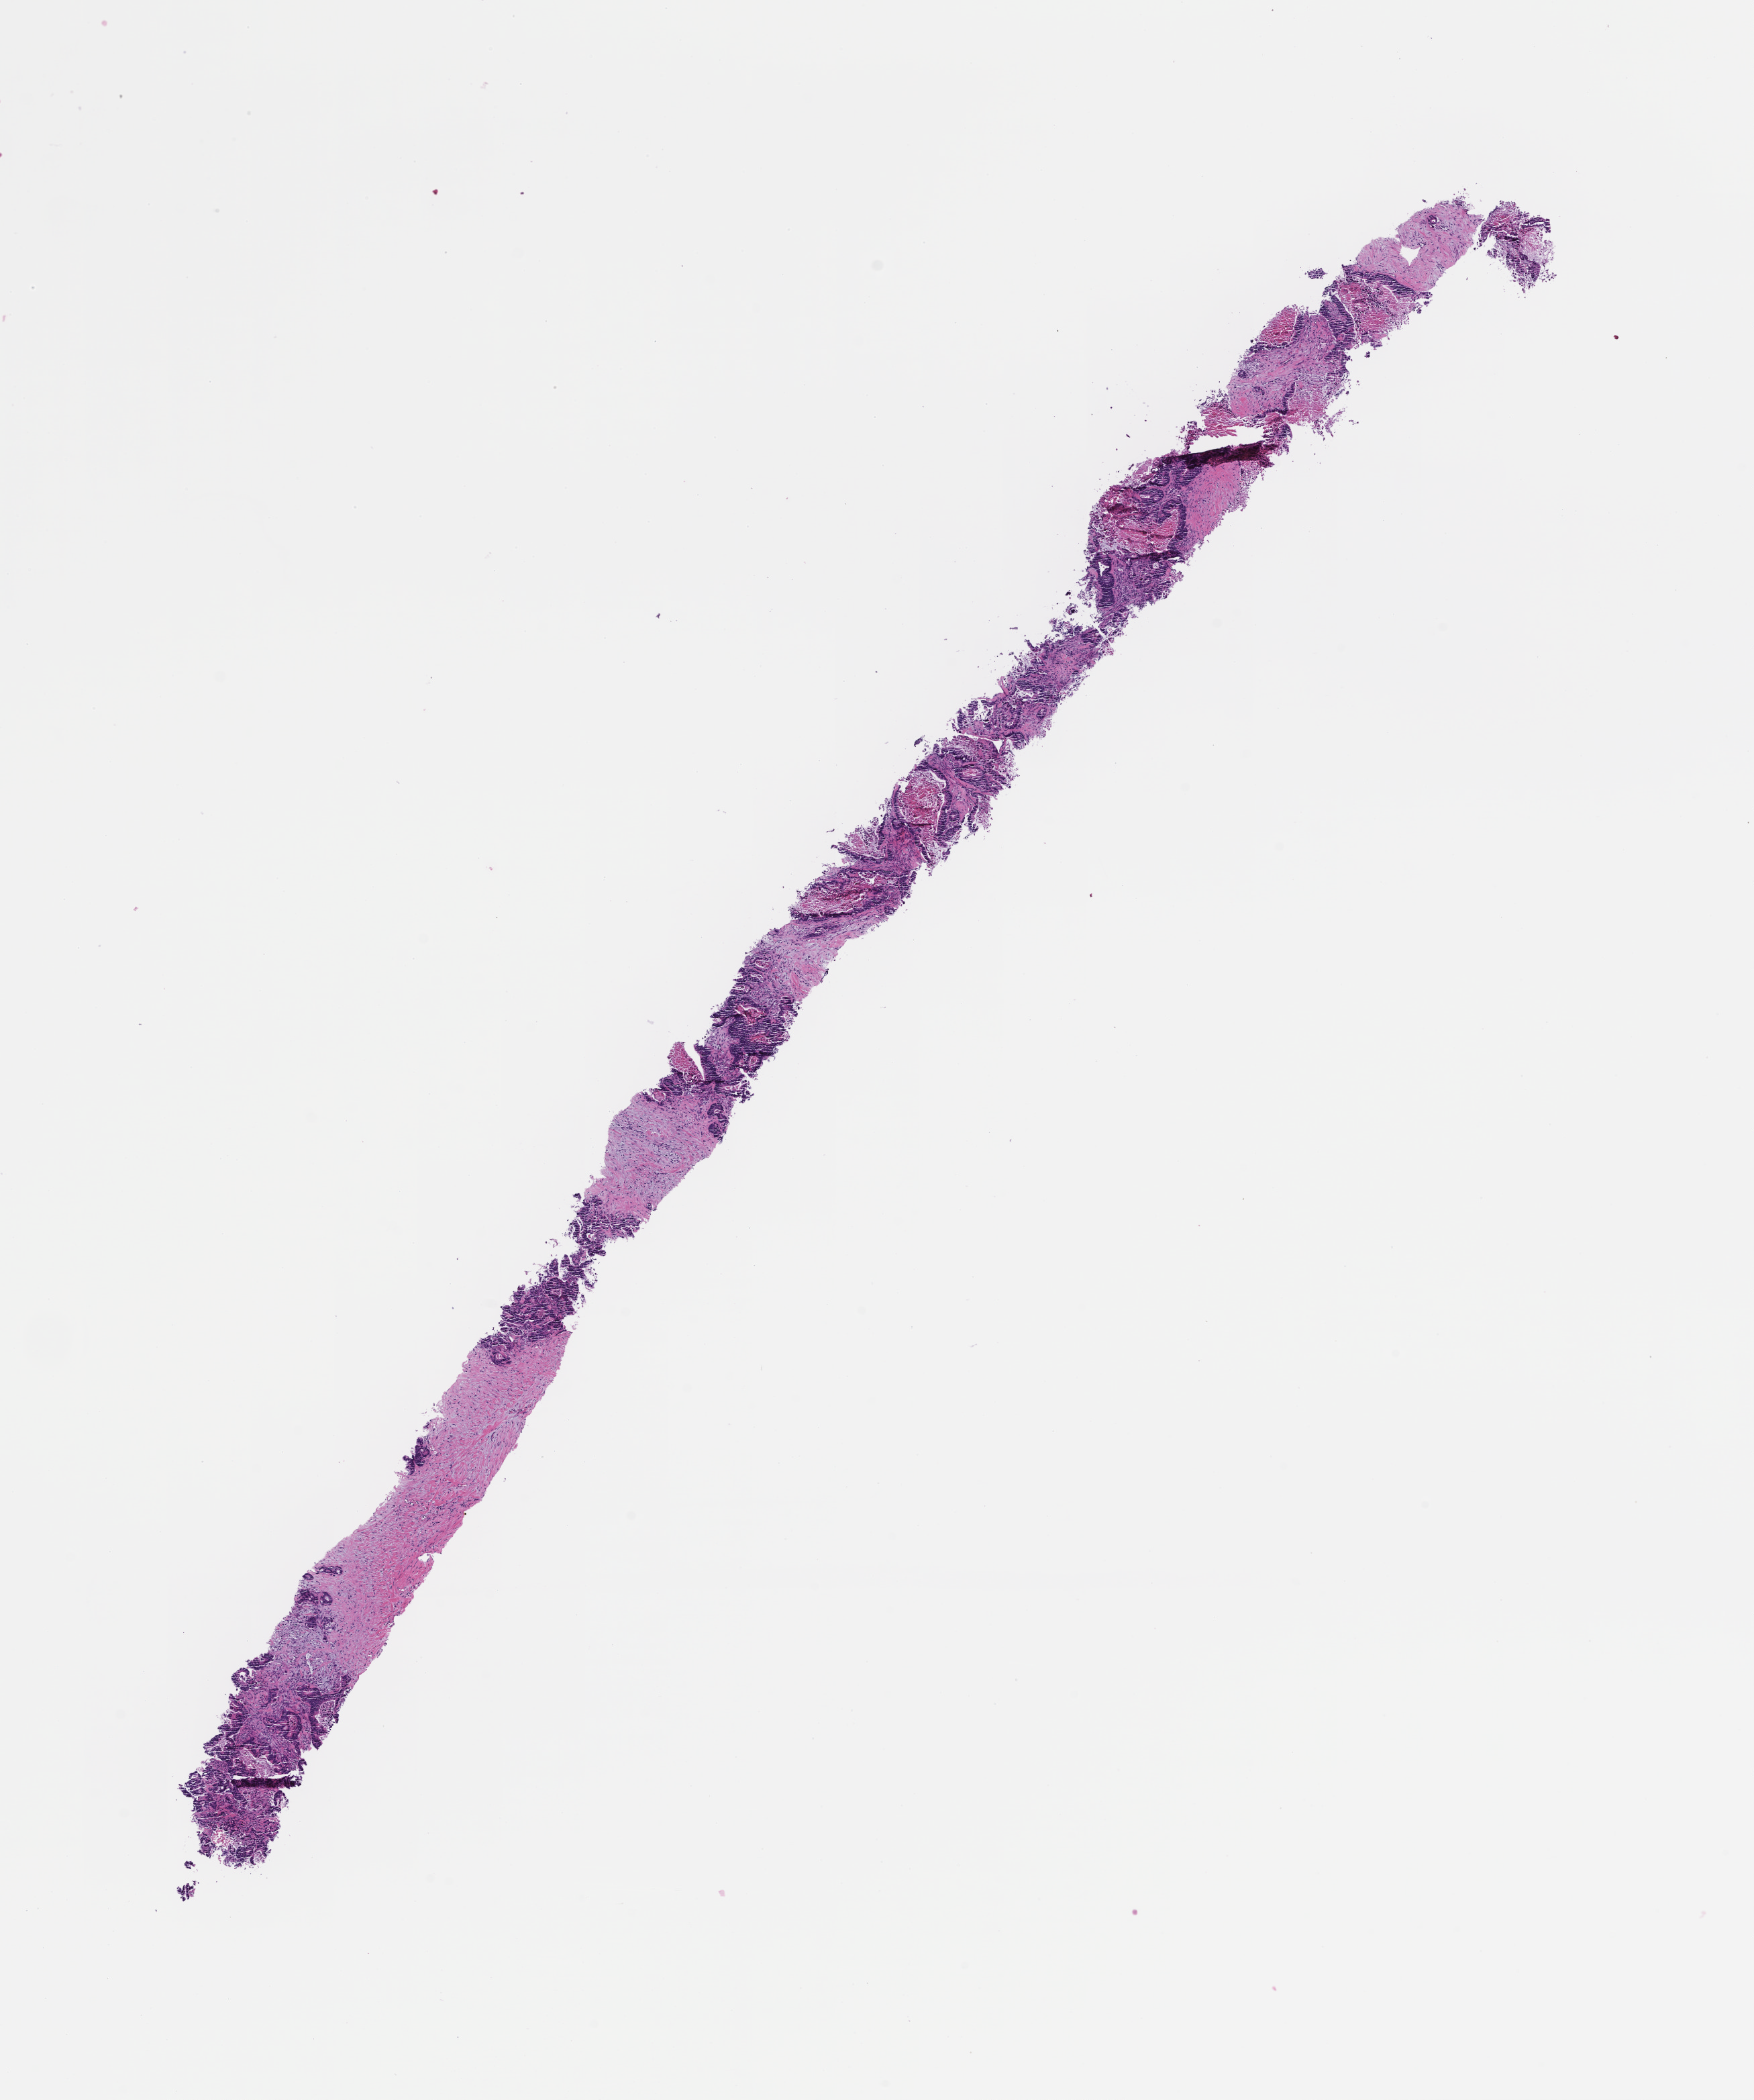
H&E whole-slide image — shown as a low-resolution overview of the whole scanned area (about 10.6 x 12.6 mm), FFPE section, tissue site: colon. Male patient.
This section: primary tumor. Diagnosis: Colorectal Carcinoma.